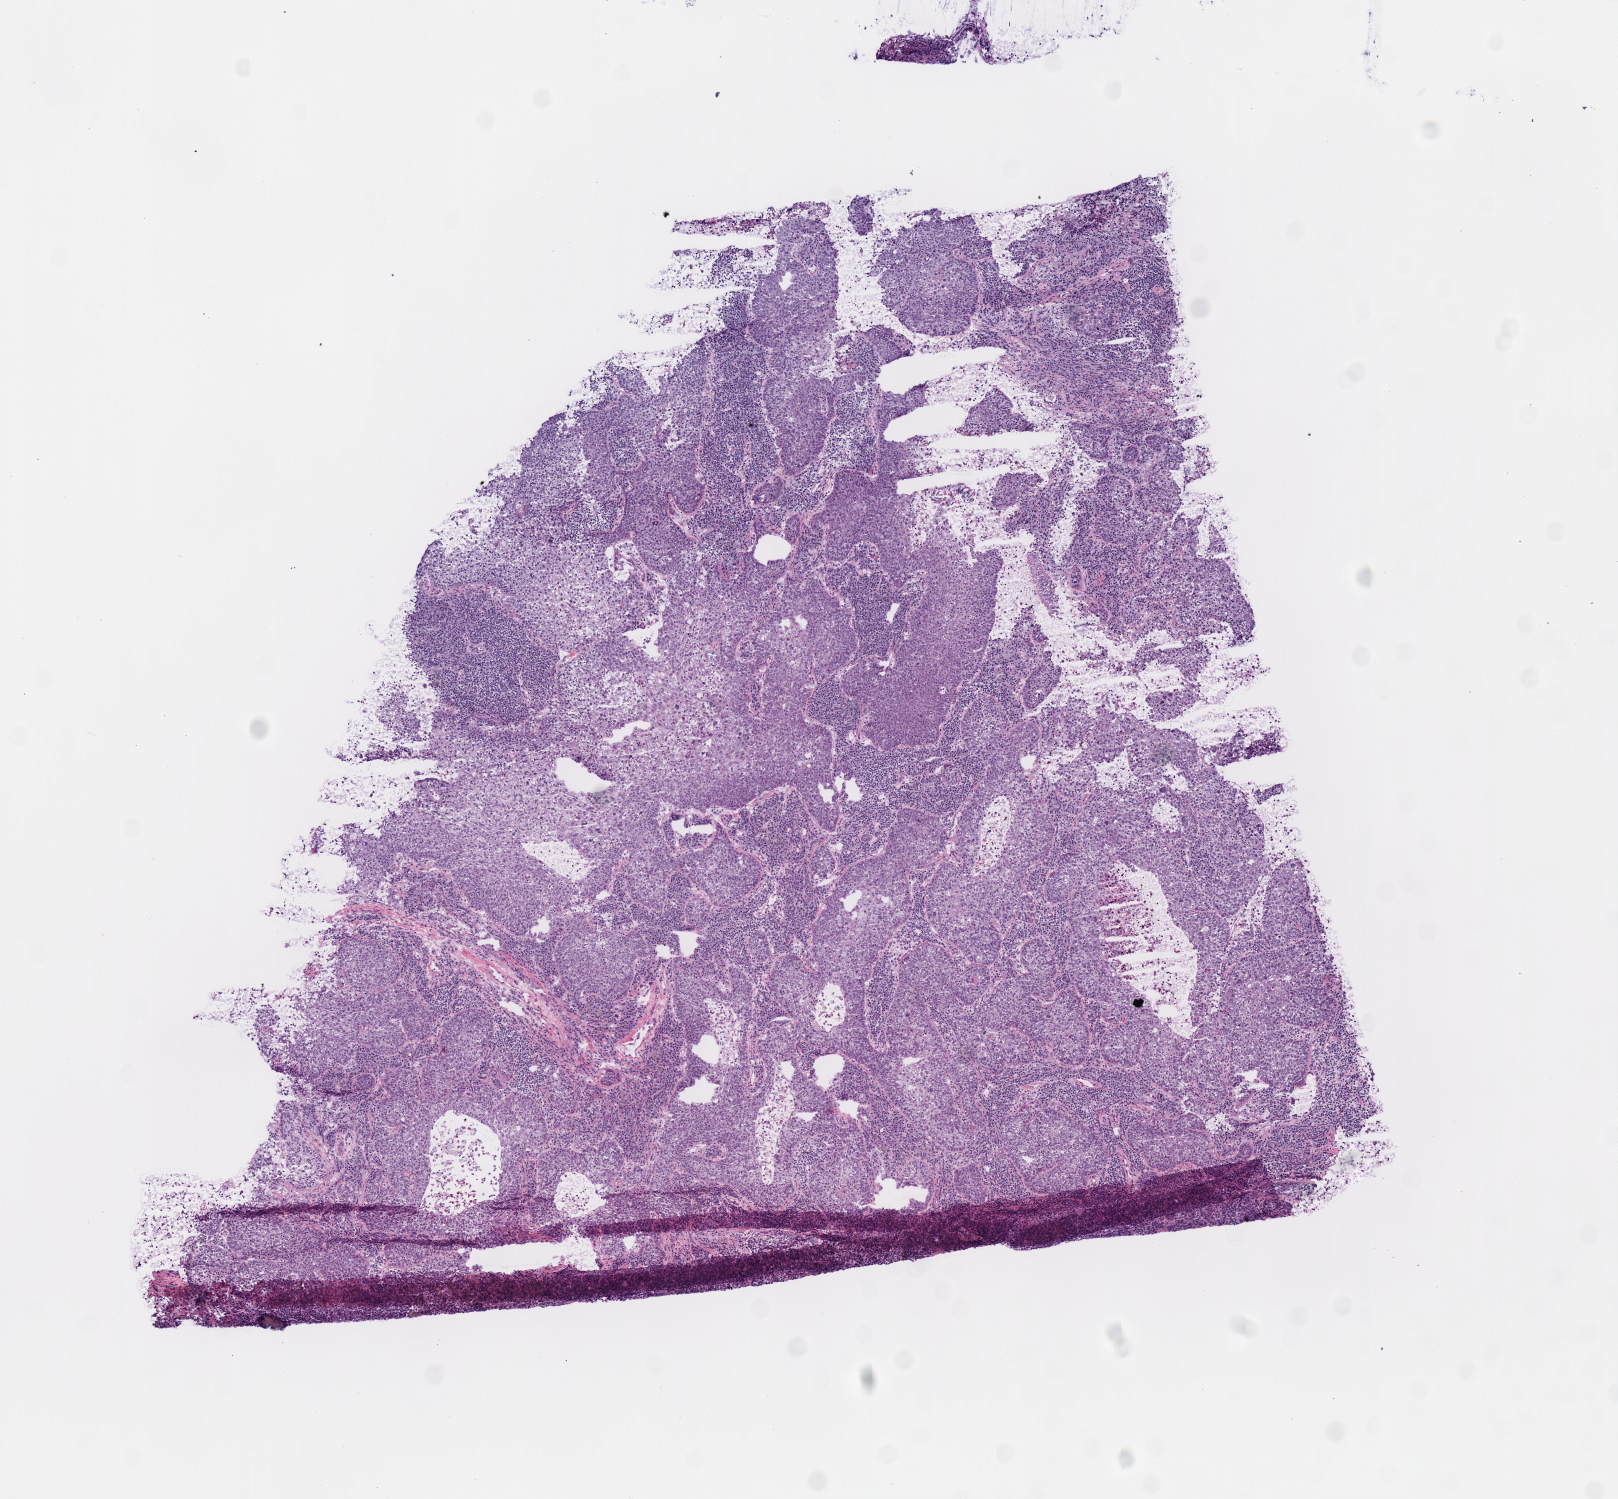
Whole-slide histology image, H&E, low-resolution overview of the scanned area, about 6.4 x 5.9 mm, frozen section, lung, primary tumour sample. Female patient; age at initial diagnosis 66 years. Slide review estimates, as recorded: tumour cells 100%, tumour nuclei 61%, normal cells 0%, stromal cells 0%, necrosis 0%. Infiltration values recorded for this section: lymphocyte infiltration 35%, monocyte infiltration 0%, neutrophil infiltration 0%.
• histologic diagnosis: Squamous cell carcinoma, NOS (upper lobe, lung)
• AJCC pathologic stage: IA (7th edition)
• laterality: right